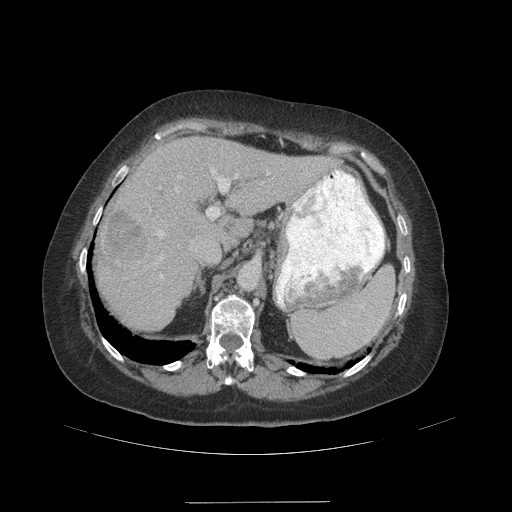
Contrast-enhanced abdominal CT (liver protocol), one axial slice; position 69 of 99 along the scan axis; 140 kVp; soft-tissue window (W 400 / L 40 HU); 2.5 mm slice thickness; 512 × 512 image matrix, field of view 440 × 440 mm. Case-level facts recorded for this patient, not image findings: diagnosis: hepatocellular carcinoma (patient treated with transarterial chemoembolisation; whether this scan precedes or follows treatment is not stated here); TNM stage (as recorded): Stage-IVA; Child-Pugh class: A.
Annotated regions visible in this slice (semi-automatic segmentation, software-assisted and operator-edited):
- liver parenchyma outside the tumour (the mass and vessels are separate outlines, so this box may not span the whole liver): bounding box <96,136,328,330> (left, top, right, bottom; pixels)
- mass: <106,211,147,262>
- liver vessels: <156,168,270,278>